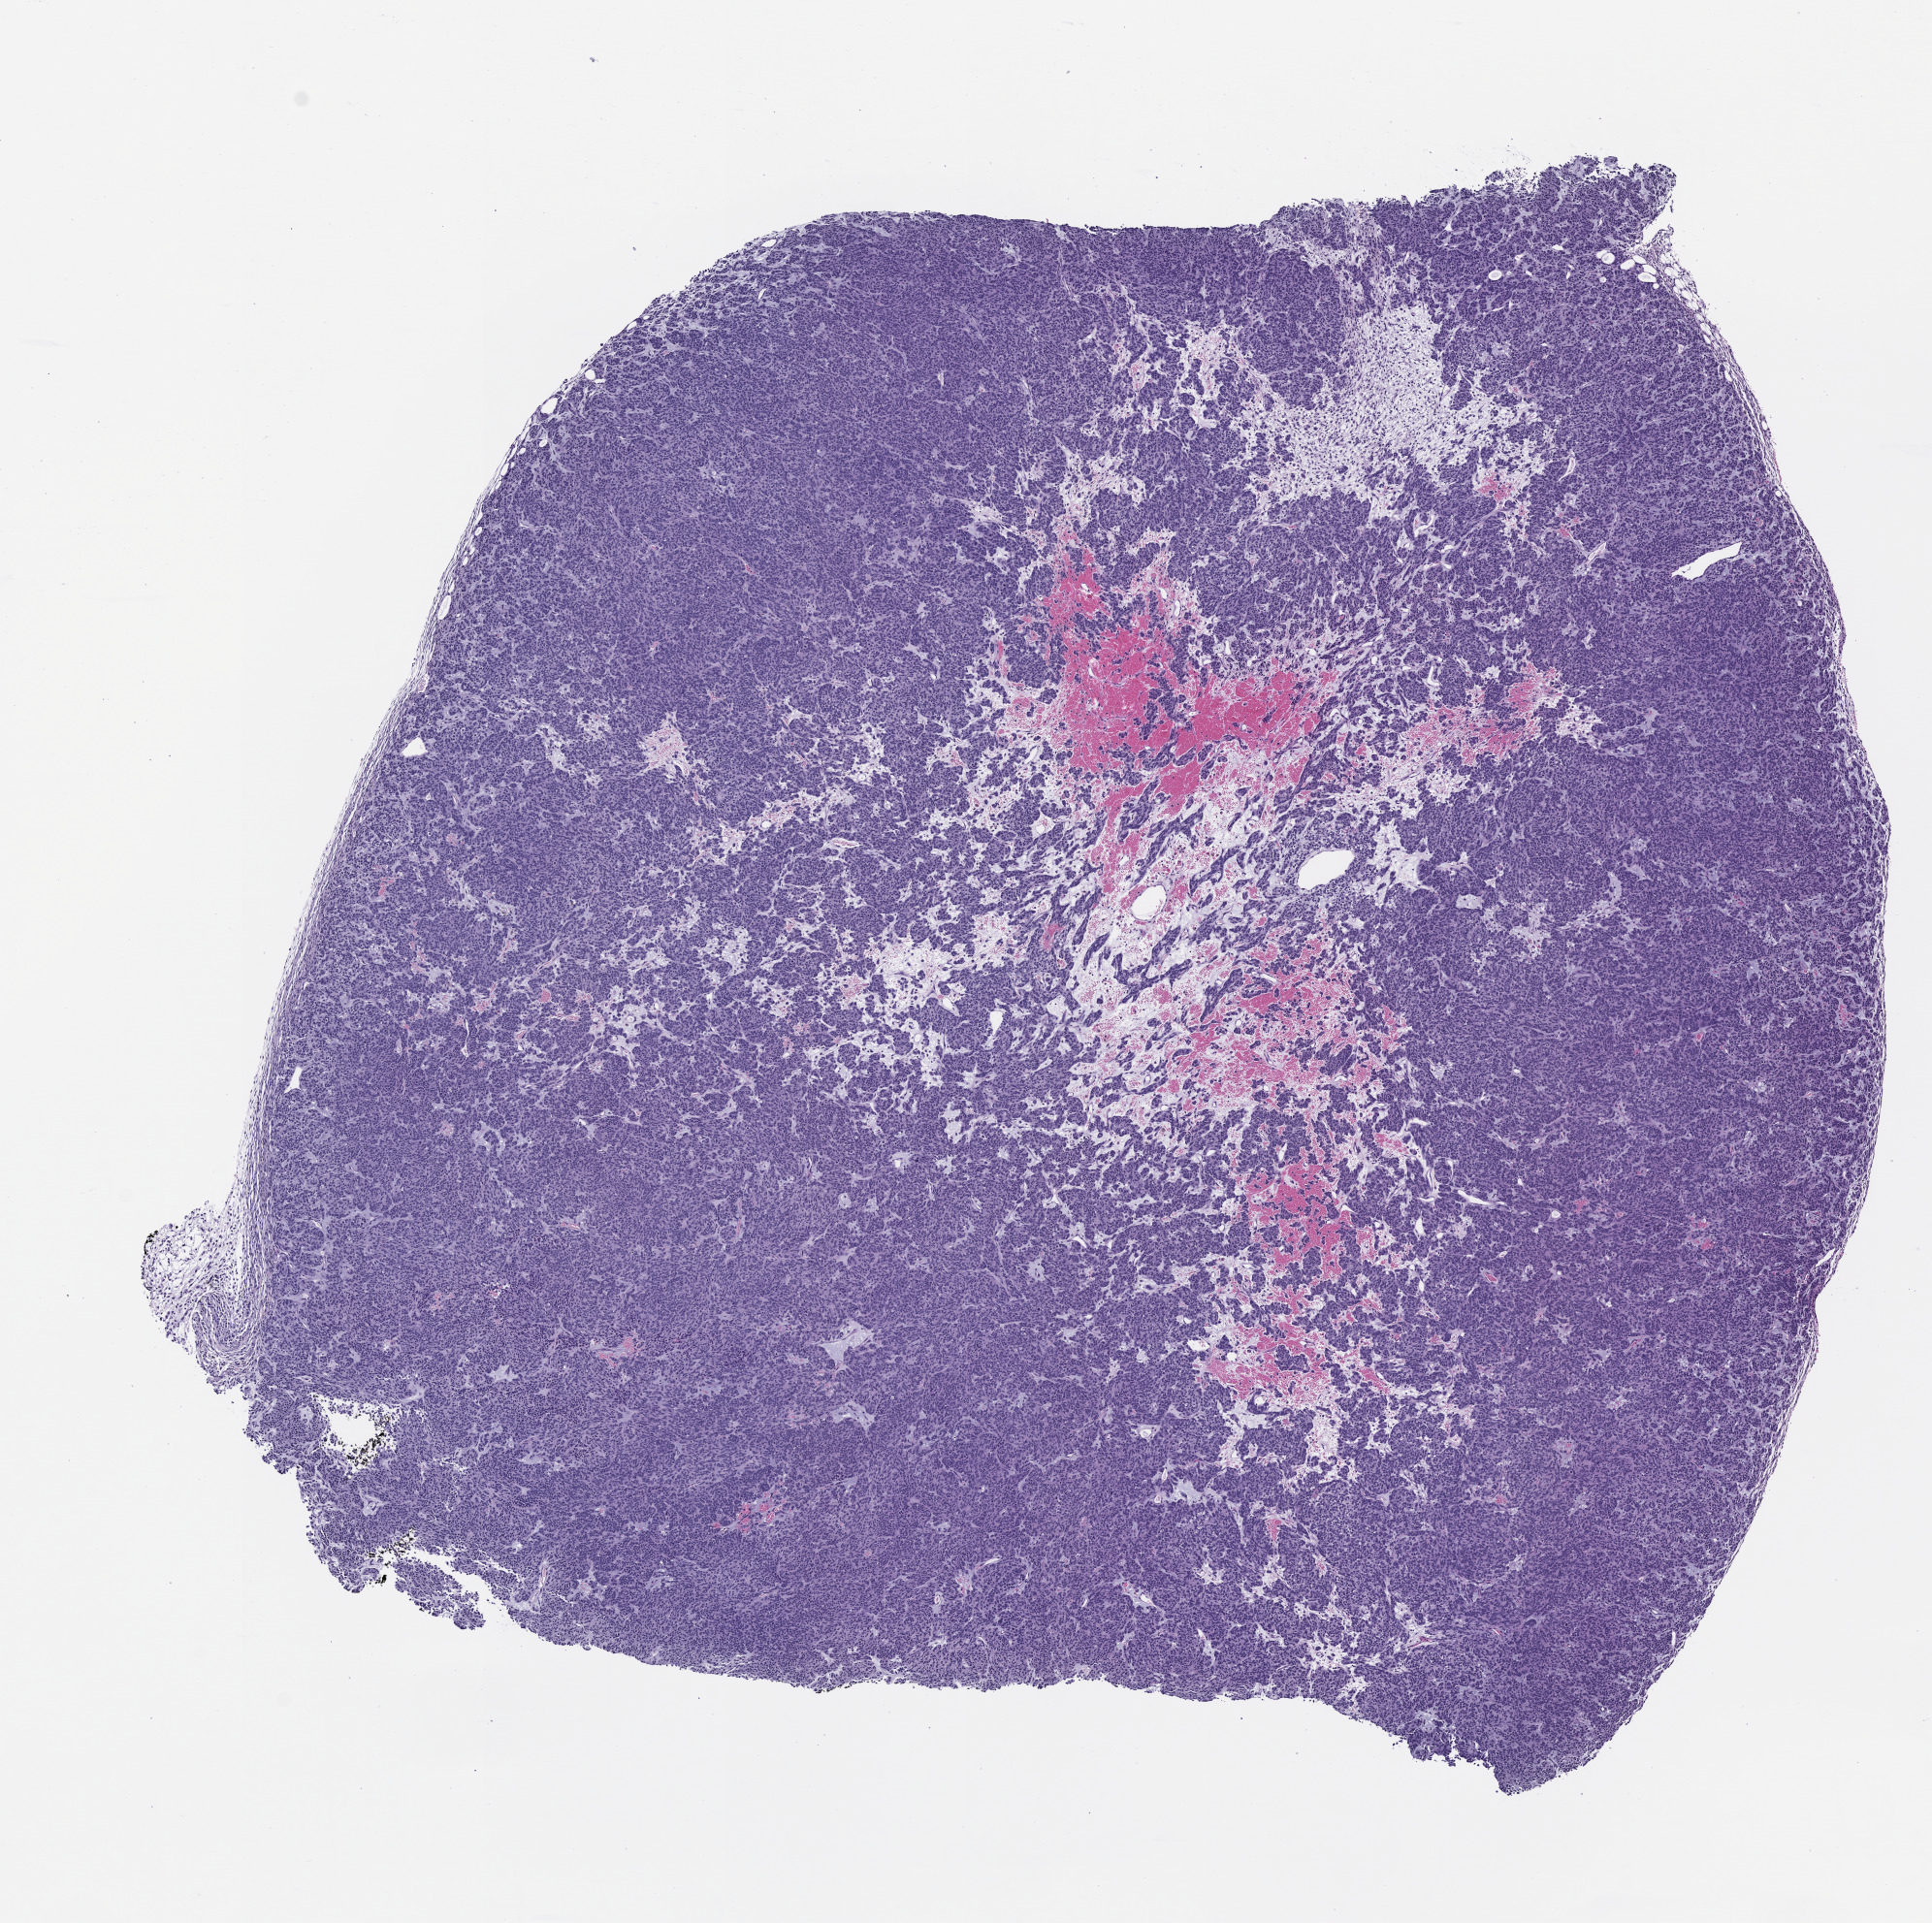
Hematoxylin and eosin (H&E) whole-slide image of a patient-derived xenograft (PDX) tumor grown in a mouse, passage 1, a low-resolution overview of the entire scanned area, about 8.0 x 8.0 mm. Formalin-fixed, paraffin-embedded (FFPE) tissue. Originating tumor site category: gastrointestinal tract.
* originating patient diagnosis: Gastrointestinal Stromal Tumor